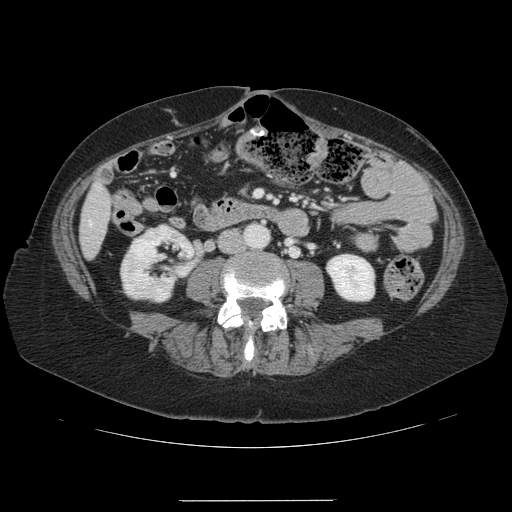
Contrast-enhanced abdominal CT, one axial slice; position 18 of 141 along the scan axis; 120 kVp; soft-tissue window (W 400 / L 40 HU); 2.5 mm slice thickness; 512 × 512 image matrix. Female patient, age 74 years. From the clinical record (not read from this slice): diagnosis: colorectal cancer liver metastases, imaged before liver resection; multiple liver metastases: yes.
Structures marked on this image (manually delineated by an expert):
- liver: bounding box <81,186,111,257> (left, top, right, bottom; pixels)
- planned liver remnant (the part of the liver to remain after resection): <85,186,111,232>